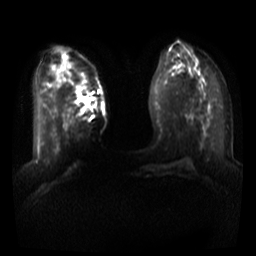
Breast MRI, one axial slice; position 14 of 44 along the scan axis; diffusion-weighted series; image 2 of 4 stored at this slice position (different b-values; order by instance number); 3 T; 5 mm slice thickness; 256 × 256 image matrix. Female patient.
Annotated regions visible in this slice (manually delineated by an expert):
- tumour on diffusion-weighted imaging: bounding box (x1, y1, x2, y2) in pixels: (80, 97, 89, 101)